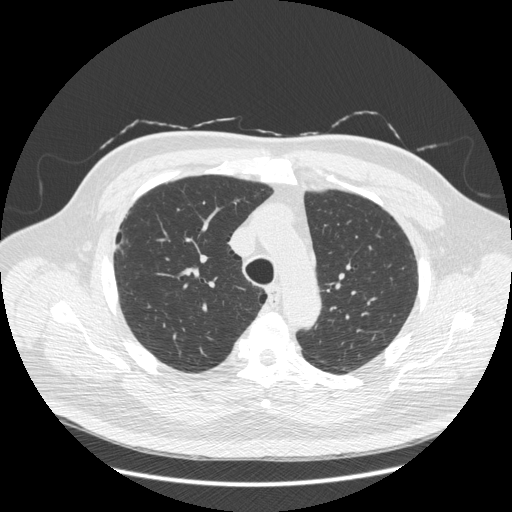
Low-dose screening chest CT, axial slice. Second screening round (one year after baseline). Lung window (W 1500 / L -600 HU). 1.25 mm slice thickness. 120 kVp. Slice 68 of 281 in the series. Male, age 66 years at enrolment. Current smoker at enrolment.
Expert reader's lesion annotation, bounding box (x1, y1, x2, y2) in pixels: (103, 214, 141, 271). The screening reader recorded 2 non-calcified nodules or masses ≥4 mm on this exam (right lower lobe, right lower lobe); which of them this box marks is not recorded.